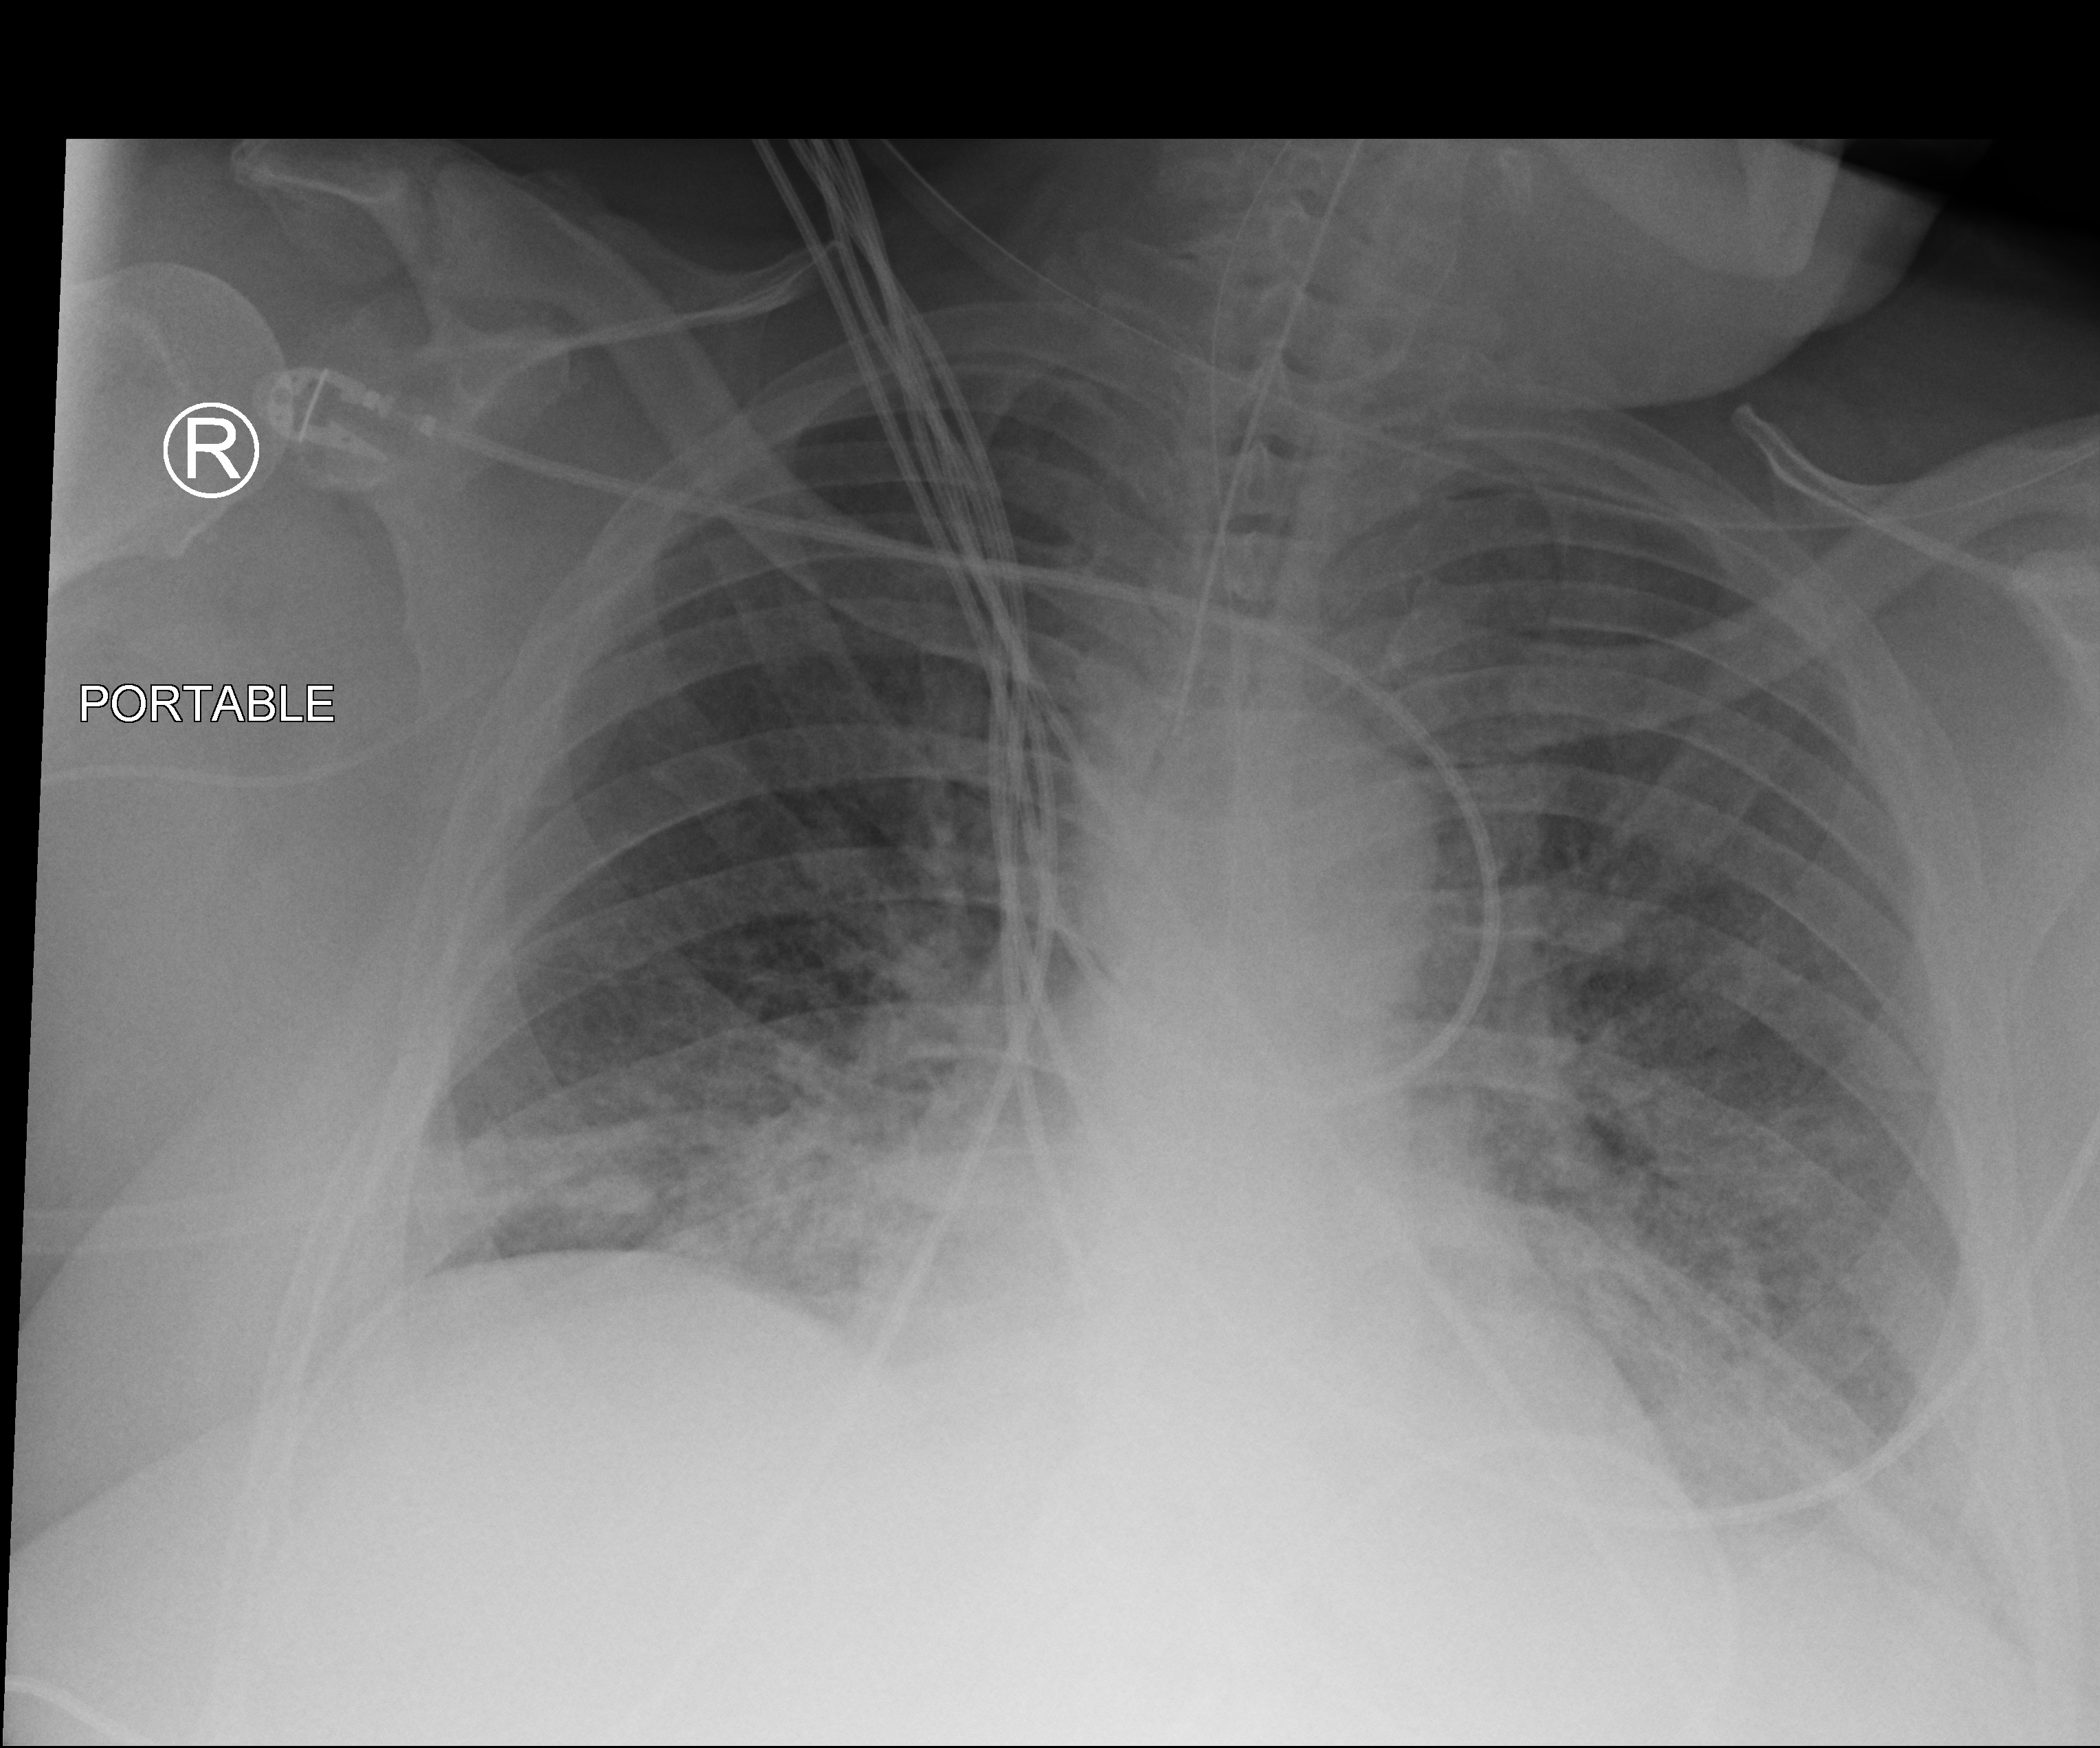
Portable chest radiograph; anteroposterior (AP) projection. Male patient hospitalised with COVID-19, age 60–74 years.
Hospital-stay facts (about this admission, not read from this image; timing relative to this image not recorded):
- mechanically ventilated during this hospital stay: yes